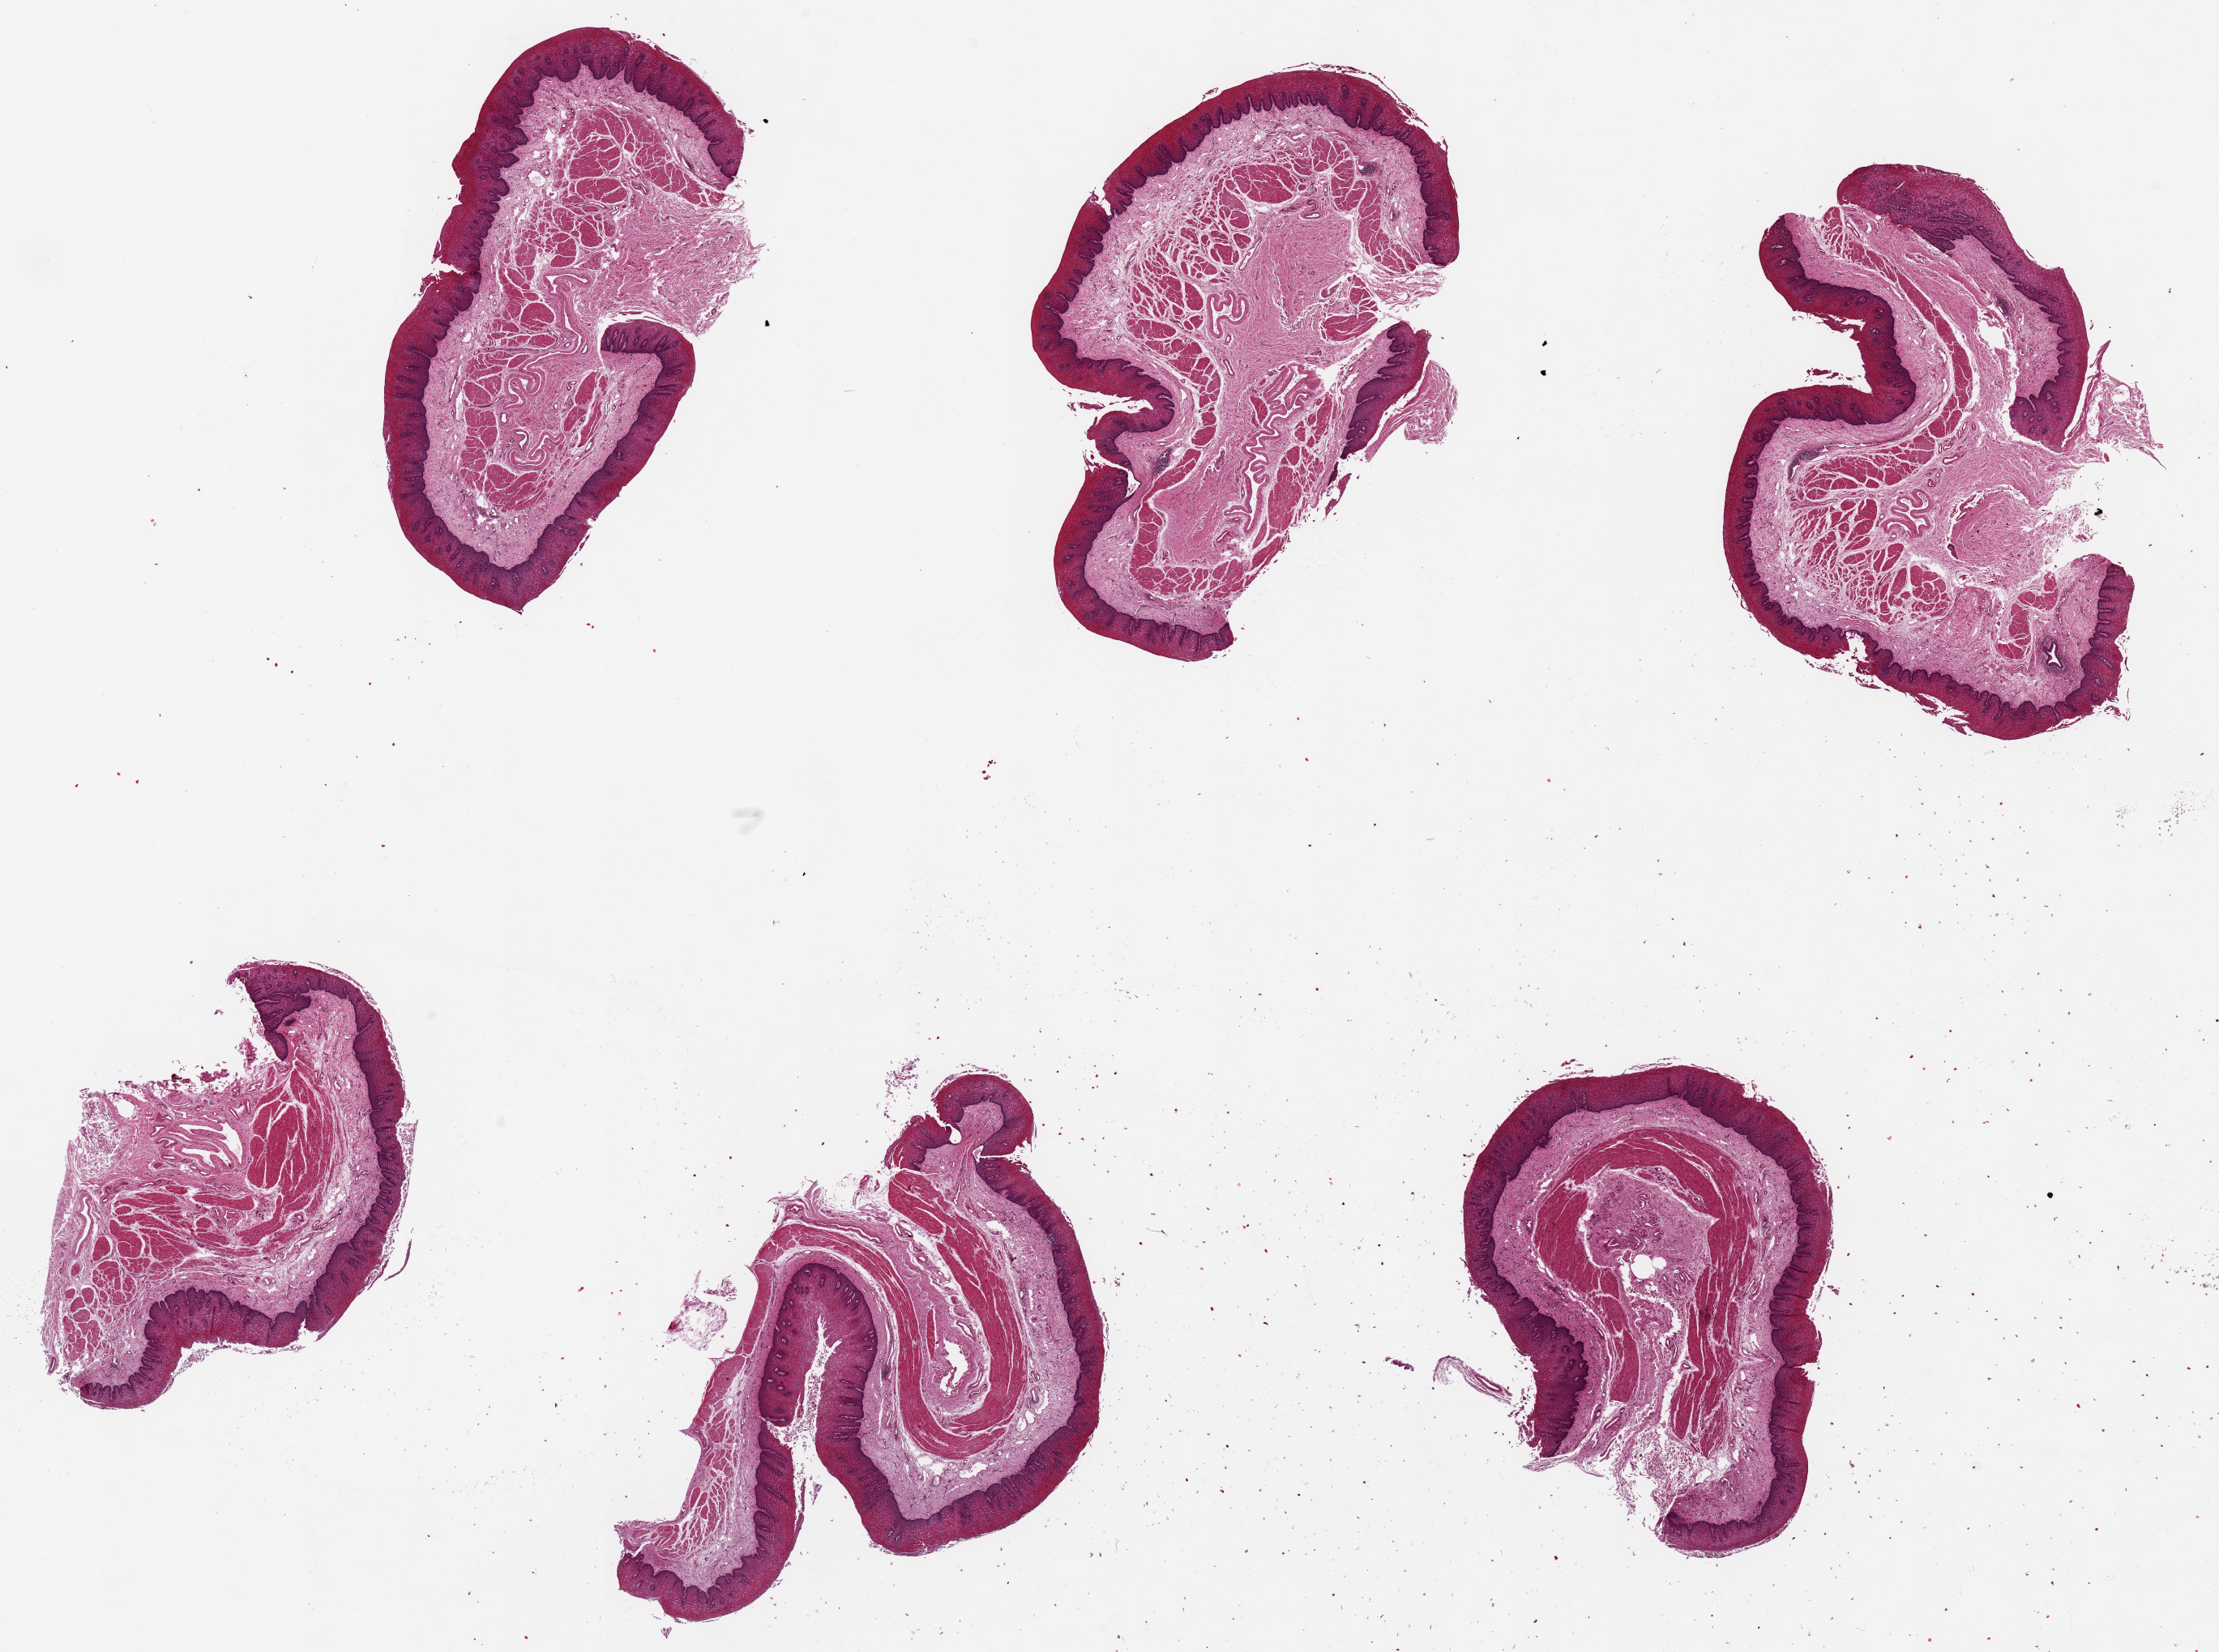
Digitized H&E-stained section, brightfield — low-resolution overview of the scanned area, about 21.7 x 16.1 mm. PAXgene-fixed paraffin-embedded (PFPE) section. Sampled site (target tissue): esophageal mucous membrane. Tissue donor sample. Donor sex: female.
Review note (as recorded): 6 pieces, up to 3x5.5mm; all with good mucosa.